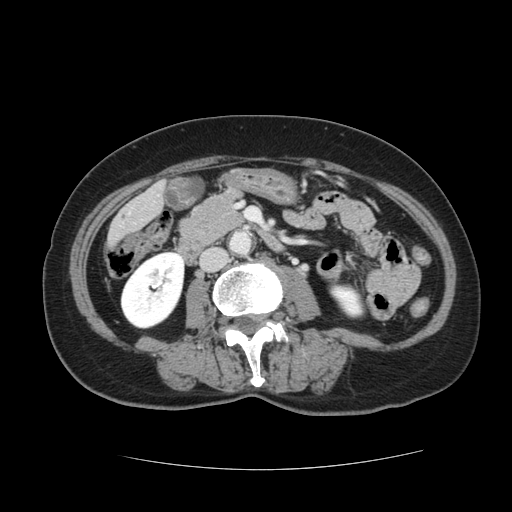
Contrast-enhanced abdominal CT, one axial slice; position 22 of 128 along the scan axis; intravenous contrast given; soft-tissue window (W 400 / L 40 HU); 2.5 mm slice thickness; 512 × 512 image matrix. Female patient, age 67 years. From the clinical record (not read from this slice): diagnosis: colorectal cancer liver metastases, imaged before liver resection; multiple liver metastases: yes; largest metastasis: 3 cm; disease in both lobes: yes.
Annotated regions visible in this slice (manually delineated by an expert):
- liver: bounding box (x1, y1, x2, y2) in pixels: (111, 186, 163, 242)
- planned liver remnant (the part of the liver to remain after resection): (110, 208, 142, 242)